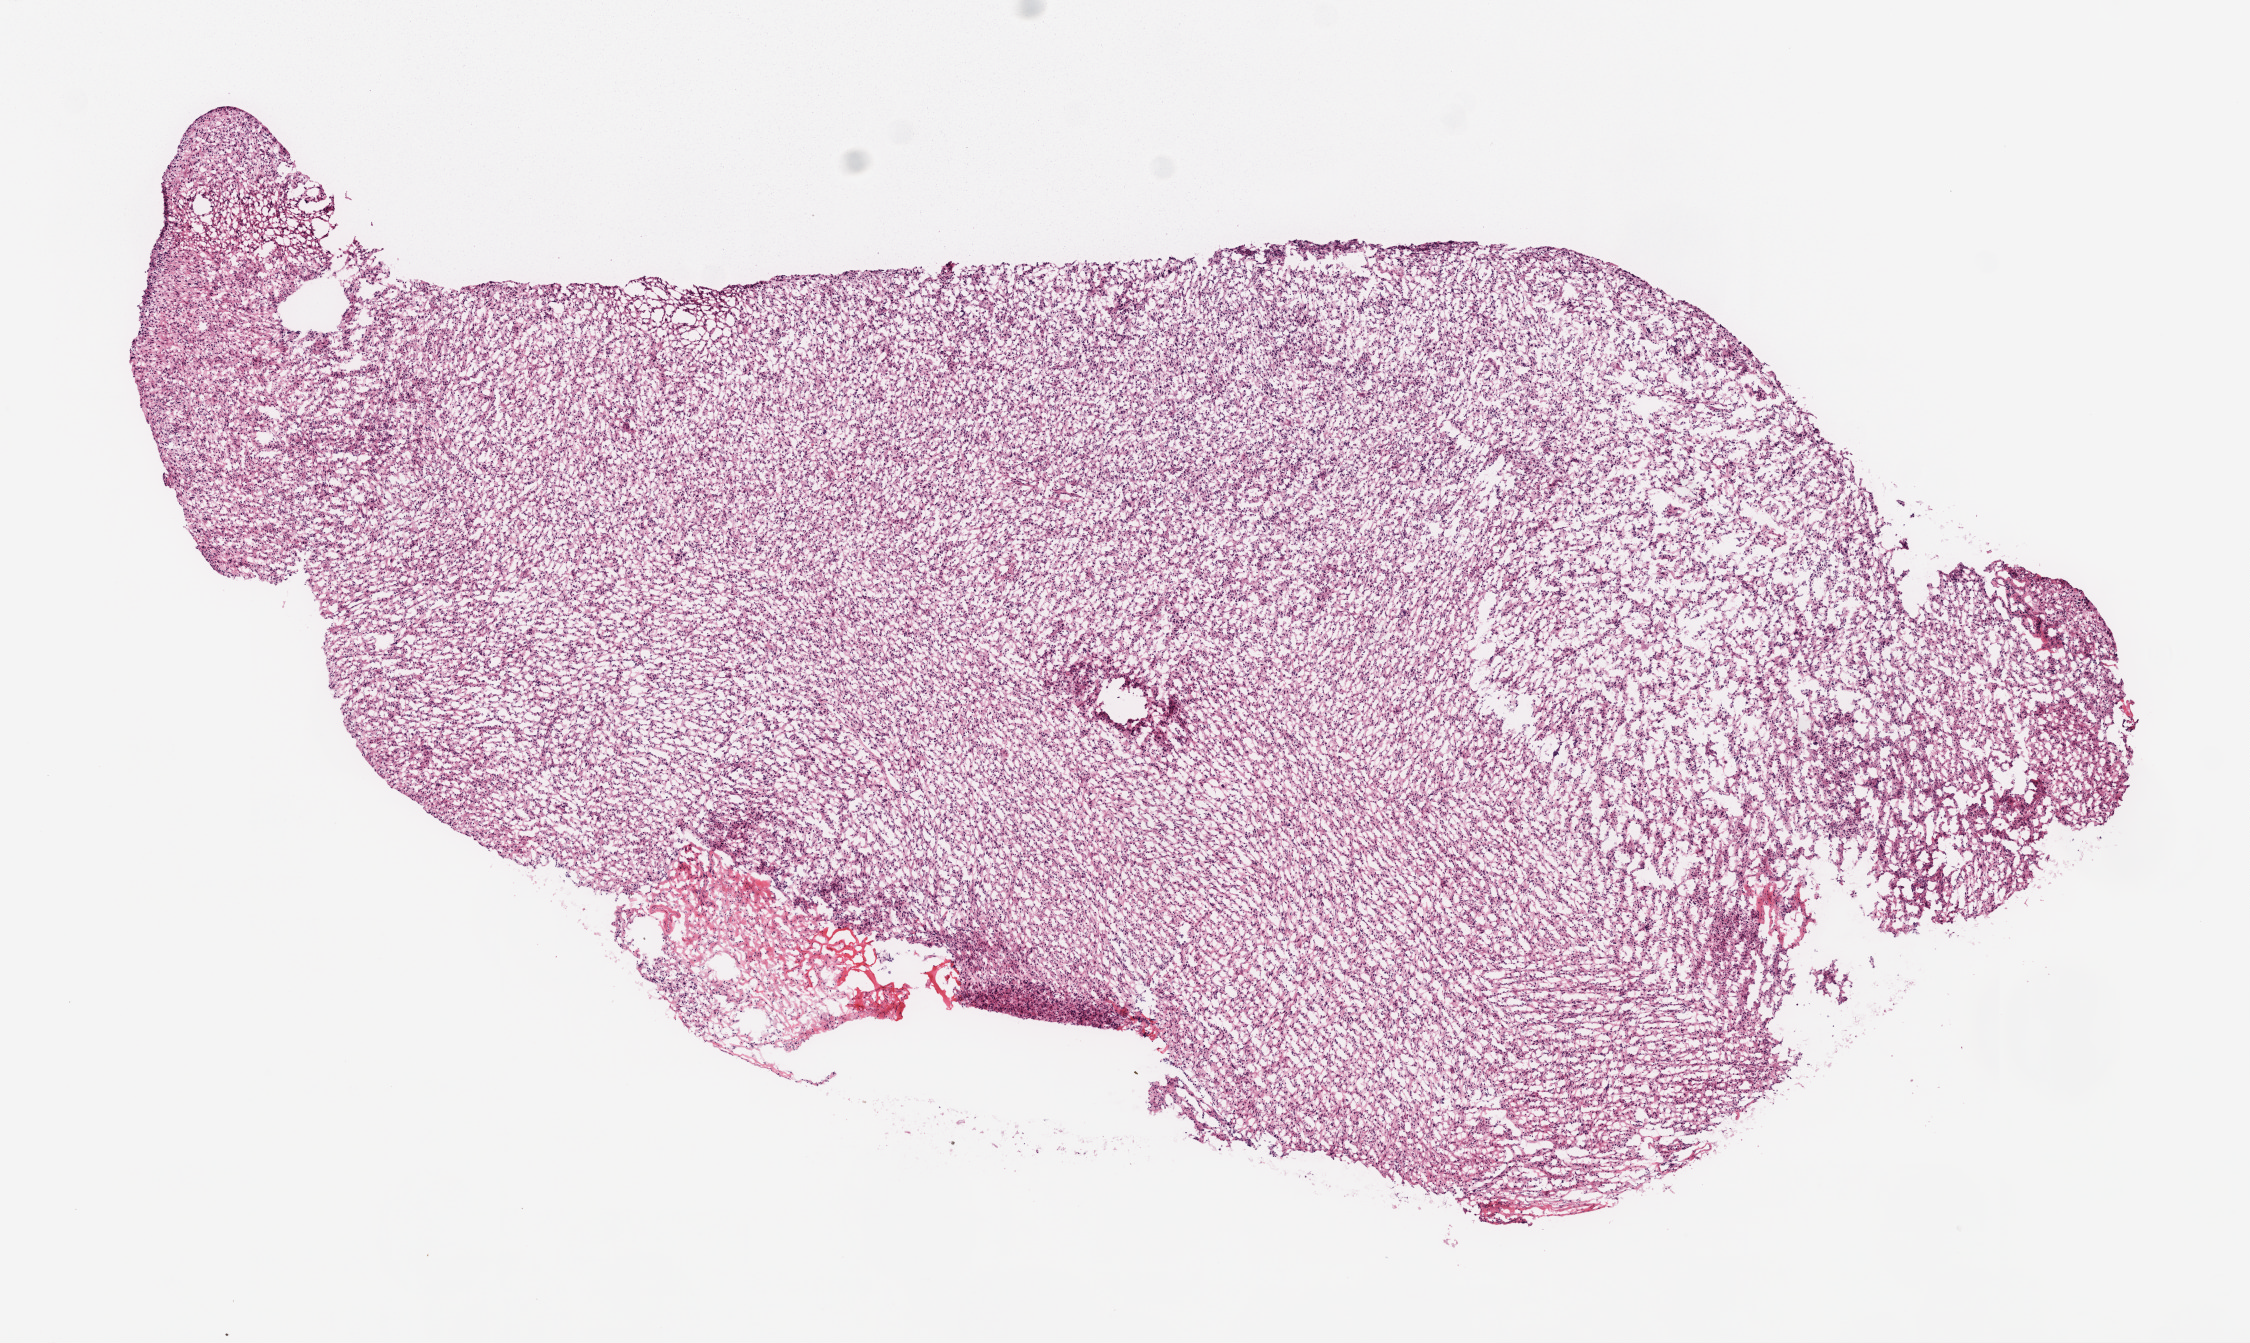
Digitized Hematoxylin and eosin (H&E) stained tissue section (whole slide) — a low-resolution overview of the entire scanned area, about 9.0 x 5.4 mm. Frozen section from the top of the tissue portion. Sample: primary tumour, brain. Patient: female, age at initial diagnosis 68 years. Slide review estimates, as recorded: tumour cells 99%, tumour nuclei 85%, normal cells 0%, stromal cells 0%, necrosis 1%.
Diagnosis: Glioblastoma.